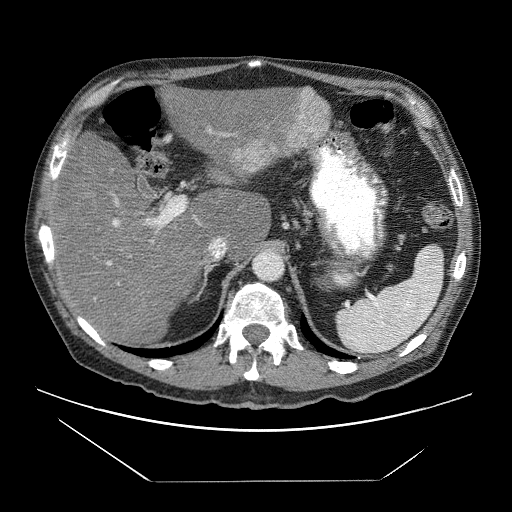
Contrast-enhanced abdominal CT (liver protocol), one axial slice. Slice 42 of 83 in the series (ordered by position). Reconstruction kernel STANDARD. 120 kVp. Soft-tissue window (W 400 / L 40 HU). 2.5 mm slice thickness. 512 × 512 image matrix. Case-level facts recorded for this patient, not image findings: diagnosis: hepatocellular carcinoma (patient treated with transarterial chemoembolisation; whether this scan precedes or follows treatment is not stated here); TNM stage (as recorded): Stage-IVB; Child-Pugh class: B; tumour differentiation: poorly differentiated; tumour nodularity: uninodular.
Annotated regions visible in this slice (semi-automatically segmented with operator editing):
- liver parenchyma outside the tumour (the mass and vessels are separate outlines, so this box may not span the whole liver): bounding box [x1, y1, x2, y2] px = [50, 78, 330, 338]
- mass: [235, 87, 331, 172]
- liver vessels: [94, 130, 229, 300]